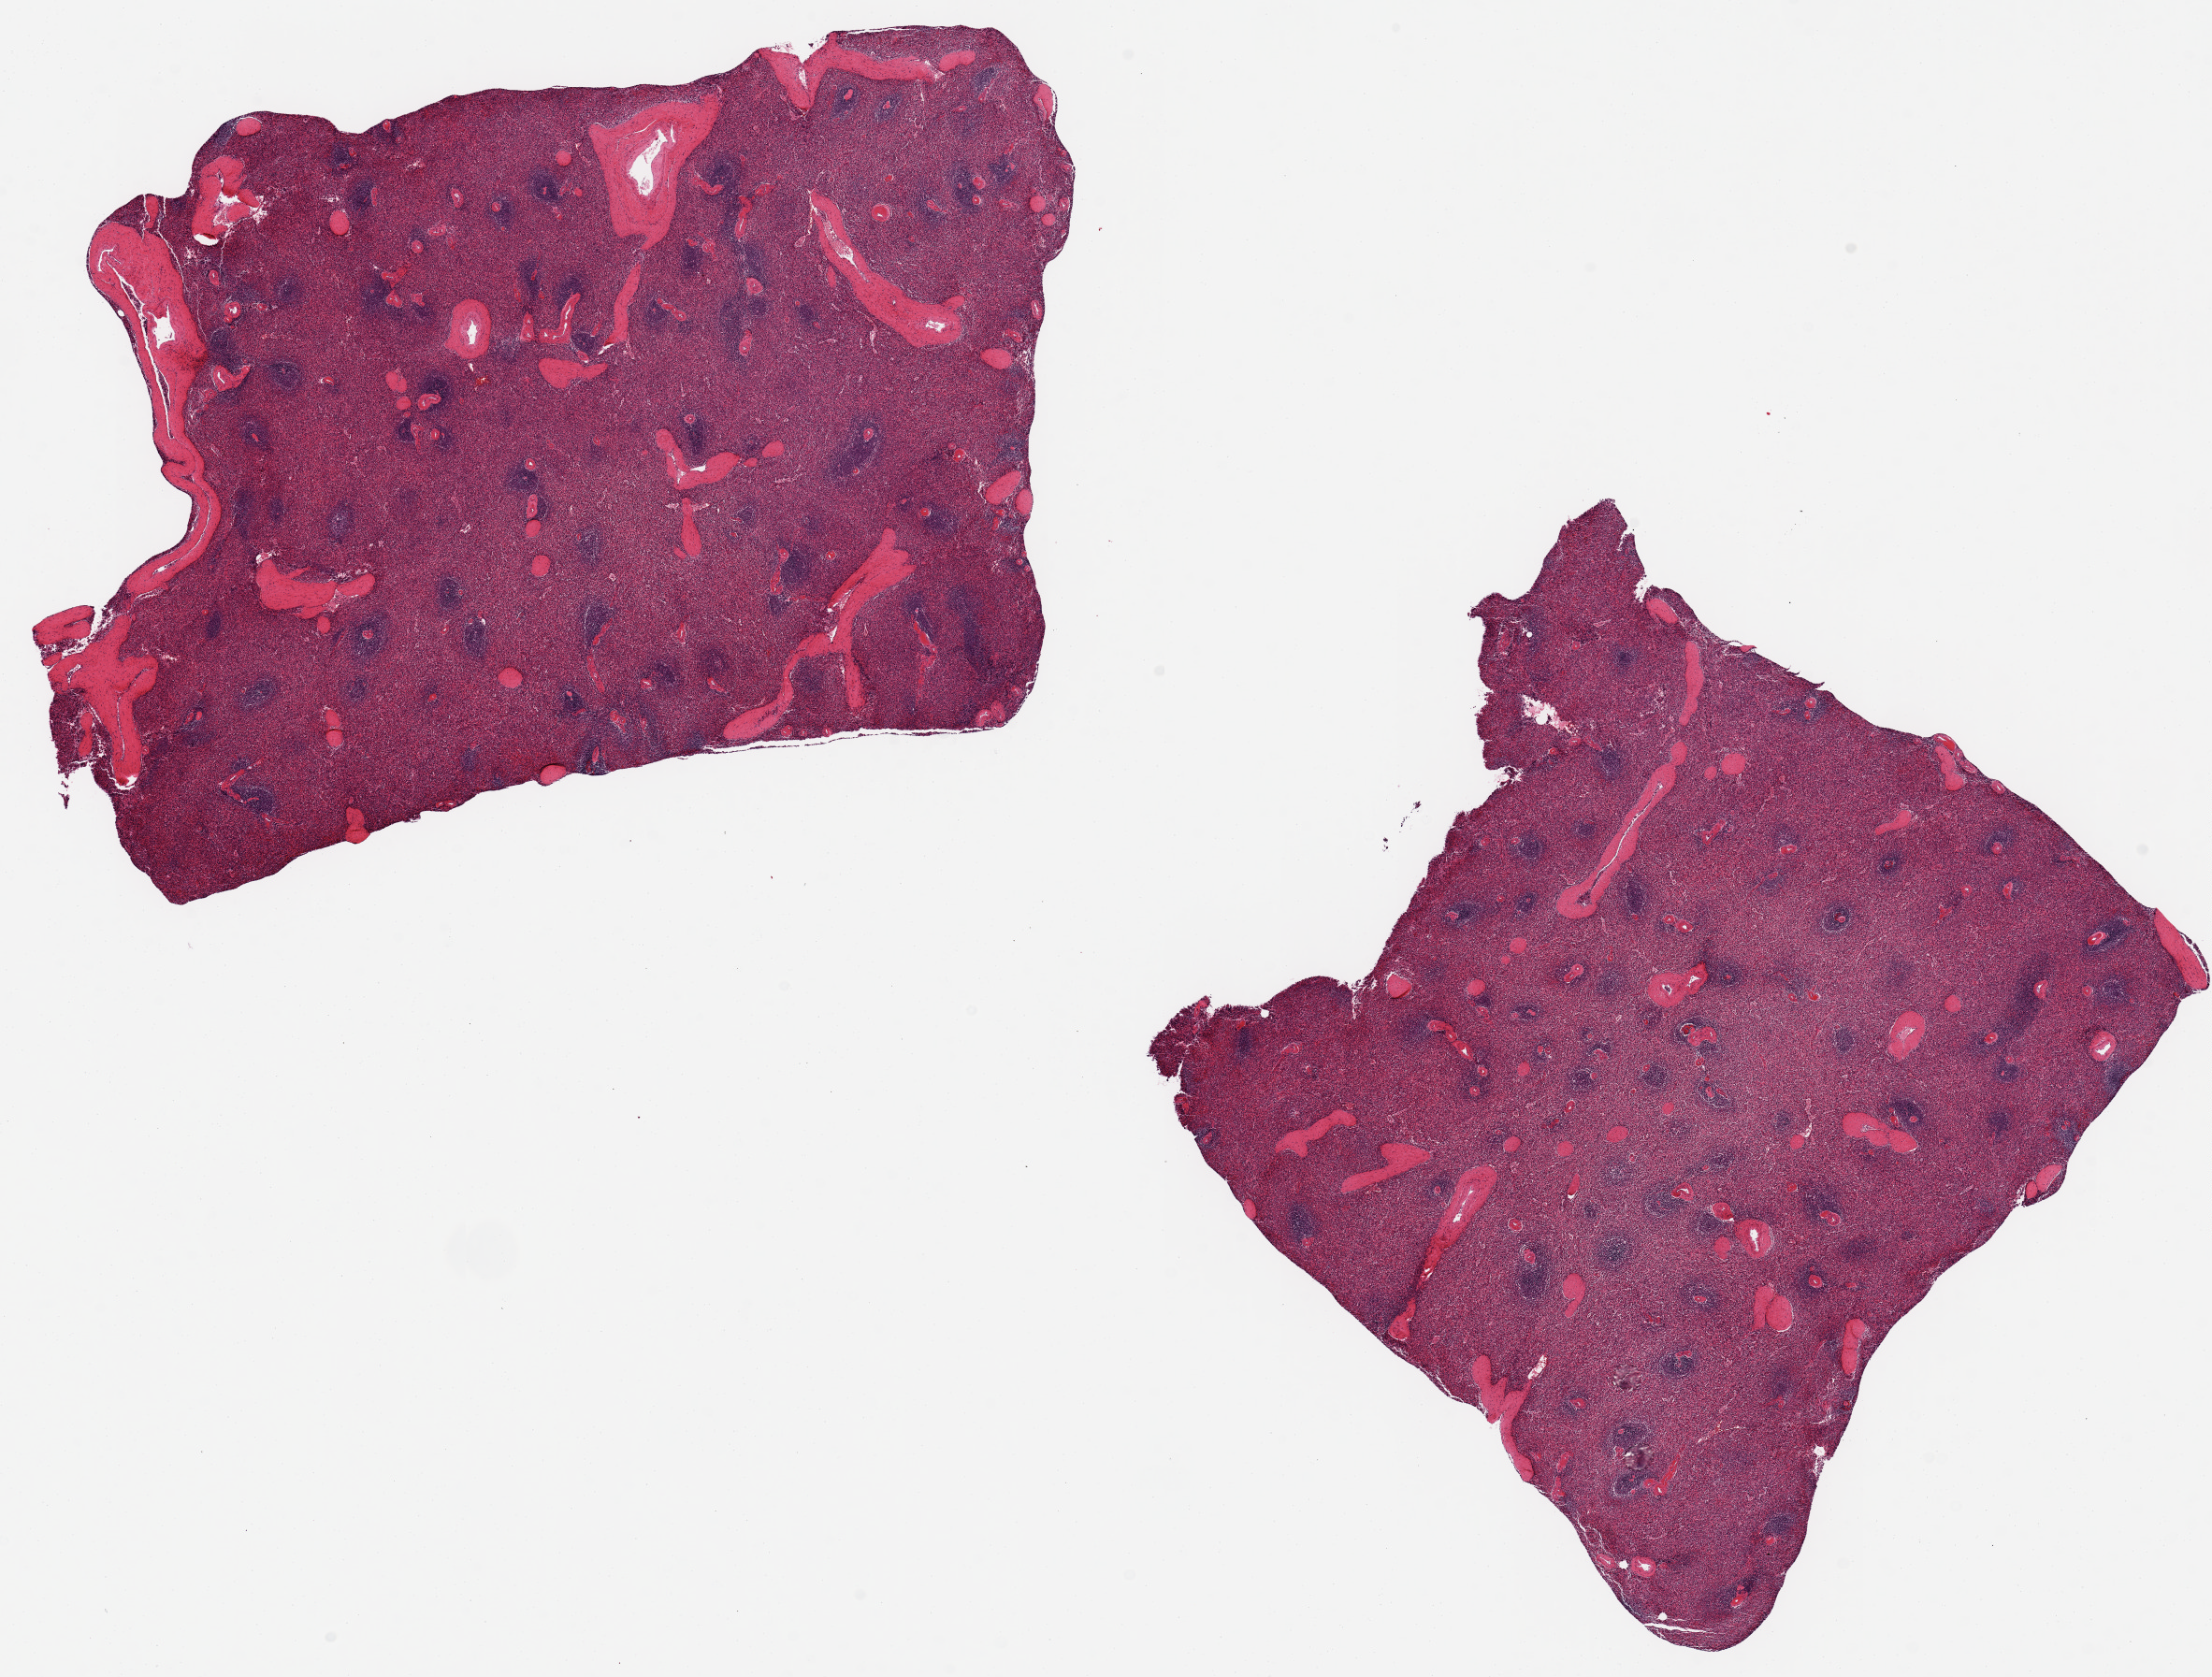
Whole-slide image, H&E stain, low-resolution overview of the scanned area, about 18.7 x 14.2 mm (from a 20x scan), PAXgene-fixed, paraffin-embedded tissue, target tissue: spleen, tissue donor sample. Donor: female.
Reviewer comment on this tissue sample: 2 pieces ~7x6mm, moderate congestion.